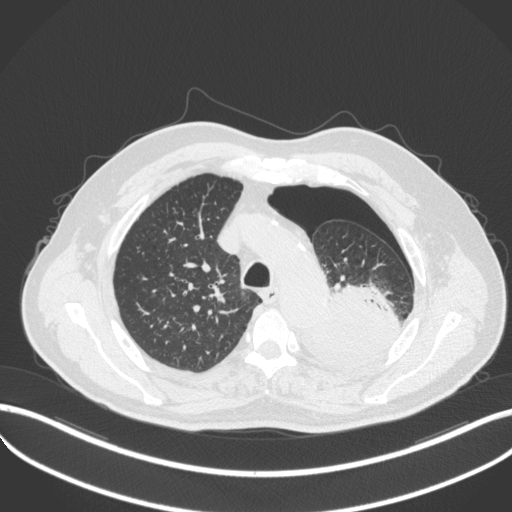
Chest CT, one axial slice; slice 384 of 466 in the series (ordered by position); 120 kVp; lung window (W 1500 / L -600 HU); 512 × 512 image matrix, field of view 400 × 400 mm. Patient: male, 76 years. From the clinical record (not read from this slice): clinical TNM (as recorded): T3 N0 M1b.
Outlined on this slice (bounding box drawn by a radiologist):
- lung tumour (recorded histology: adenocarcinoma): bounding box (x1, y1, x2, y2) in pixels: (302, 278, 401, 371)